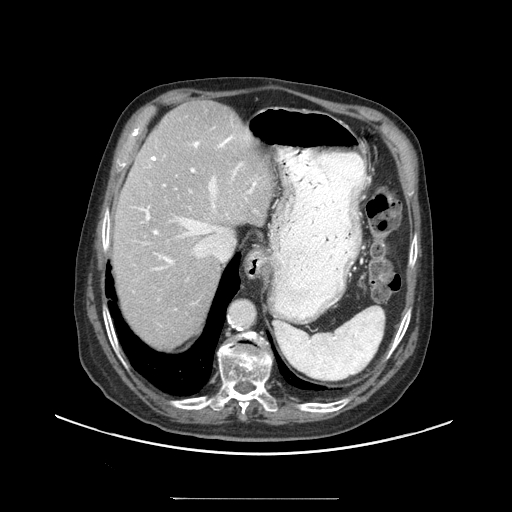
Contrast-enhanced abdominal CT (liver protocol), one axial slice; position 75 of 97 along the scan axis; reconstruction kernel STANDARD; 140 kVp; soft-tissue window (W 400 / L 40 HU); 2.5 mm slice thickness; 512 × 512 image matrix, field of view 450 × 450 mm. Case-level facts recorded for this patient, not image findings: diagnosis: hepatocellular carcinoma (patient treated with transarterial chemoembolisation; whether this scan precedes or follows treatment is not stated here); TNM stage (as recorded): Stage-IIIC; Child-Pugh class: A; tumour differentiation: well differentiated; tumour nodularity: uninodular.
Structures marked on this image (semi-automatically segmented with operator editing):
- abdominal aorta: box from (x=230, y=300) to (x=256, y=328) px
- liver parenchyma outside the tumour (the mass and vessels are separate outlines, so this box may not span the whole liver): (x=112, y=100)–(x=272, y=348)
- liver vessels: (x=133, y=135)–(x=257, y=292)